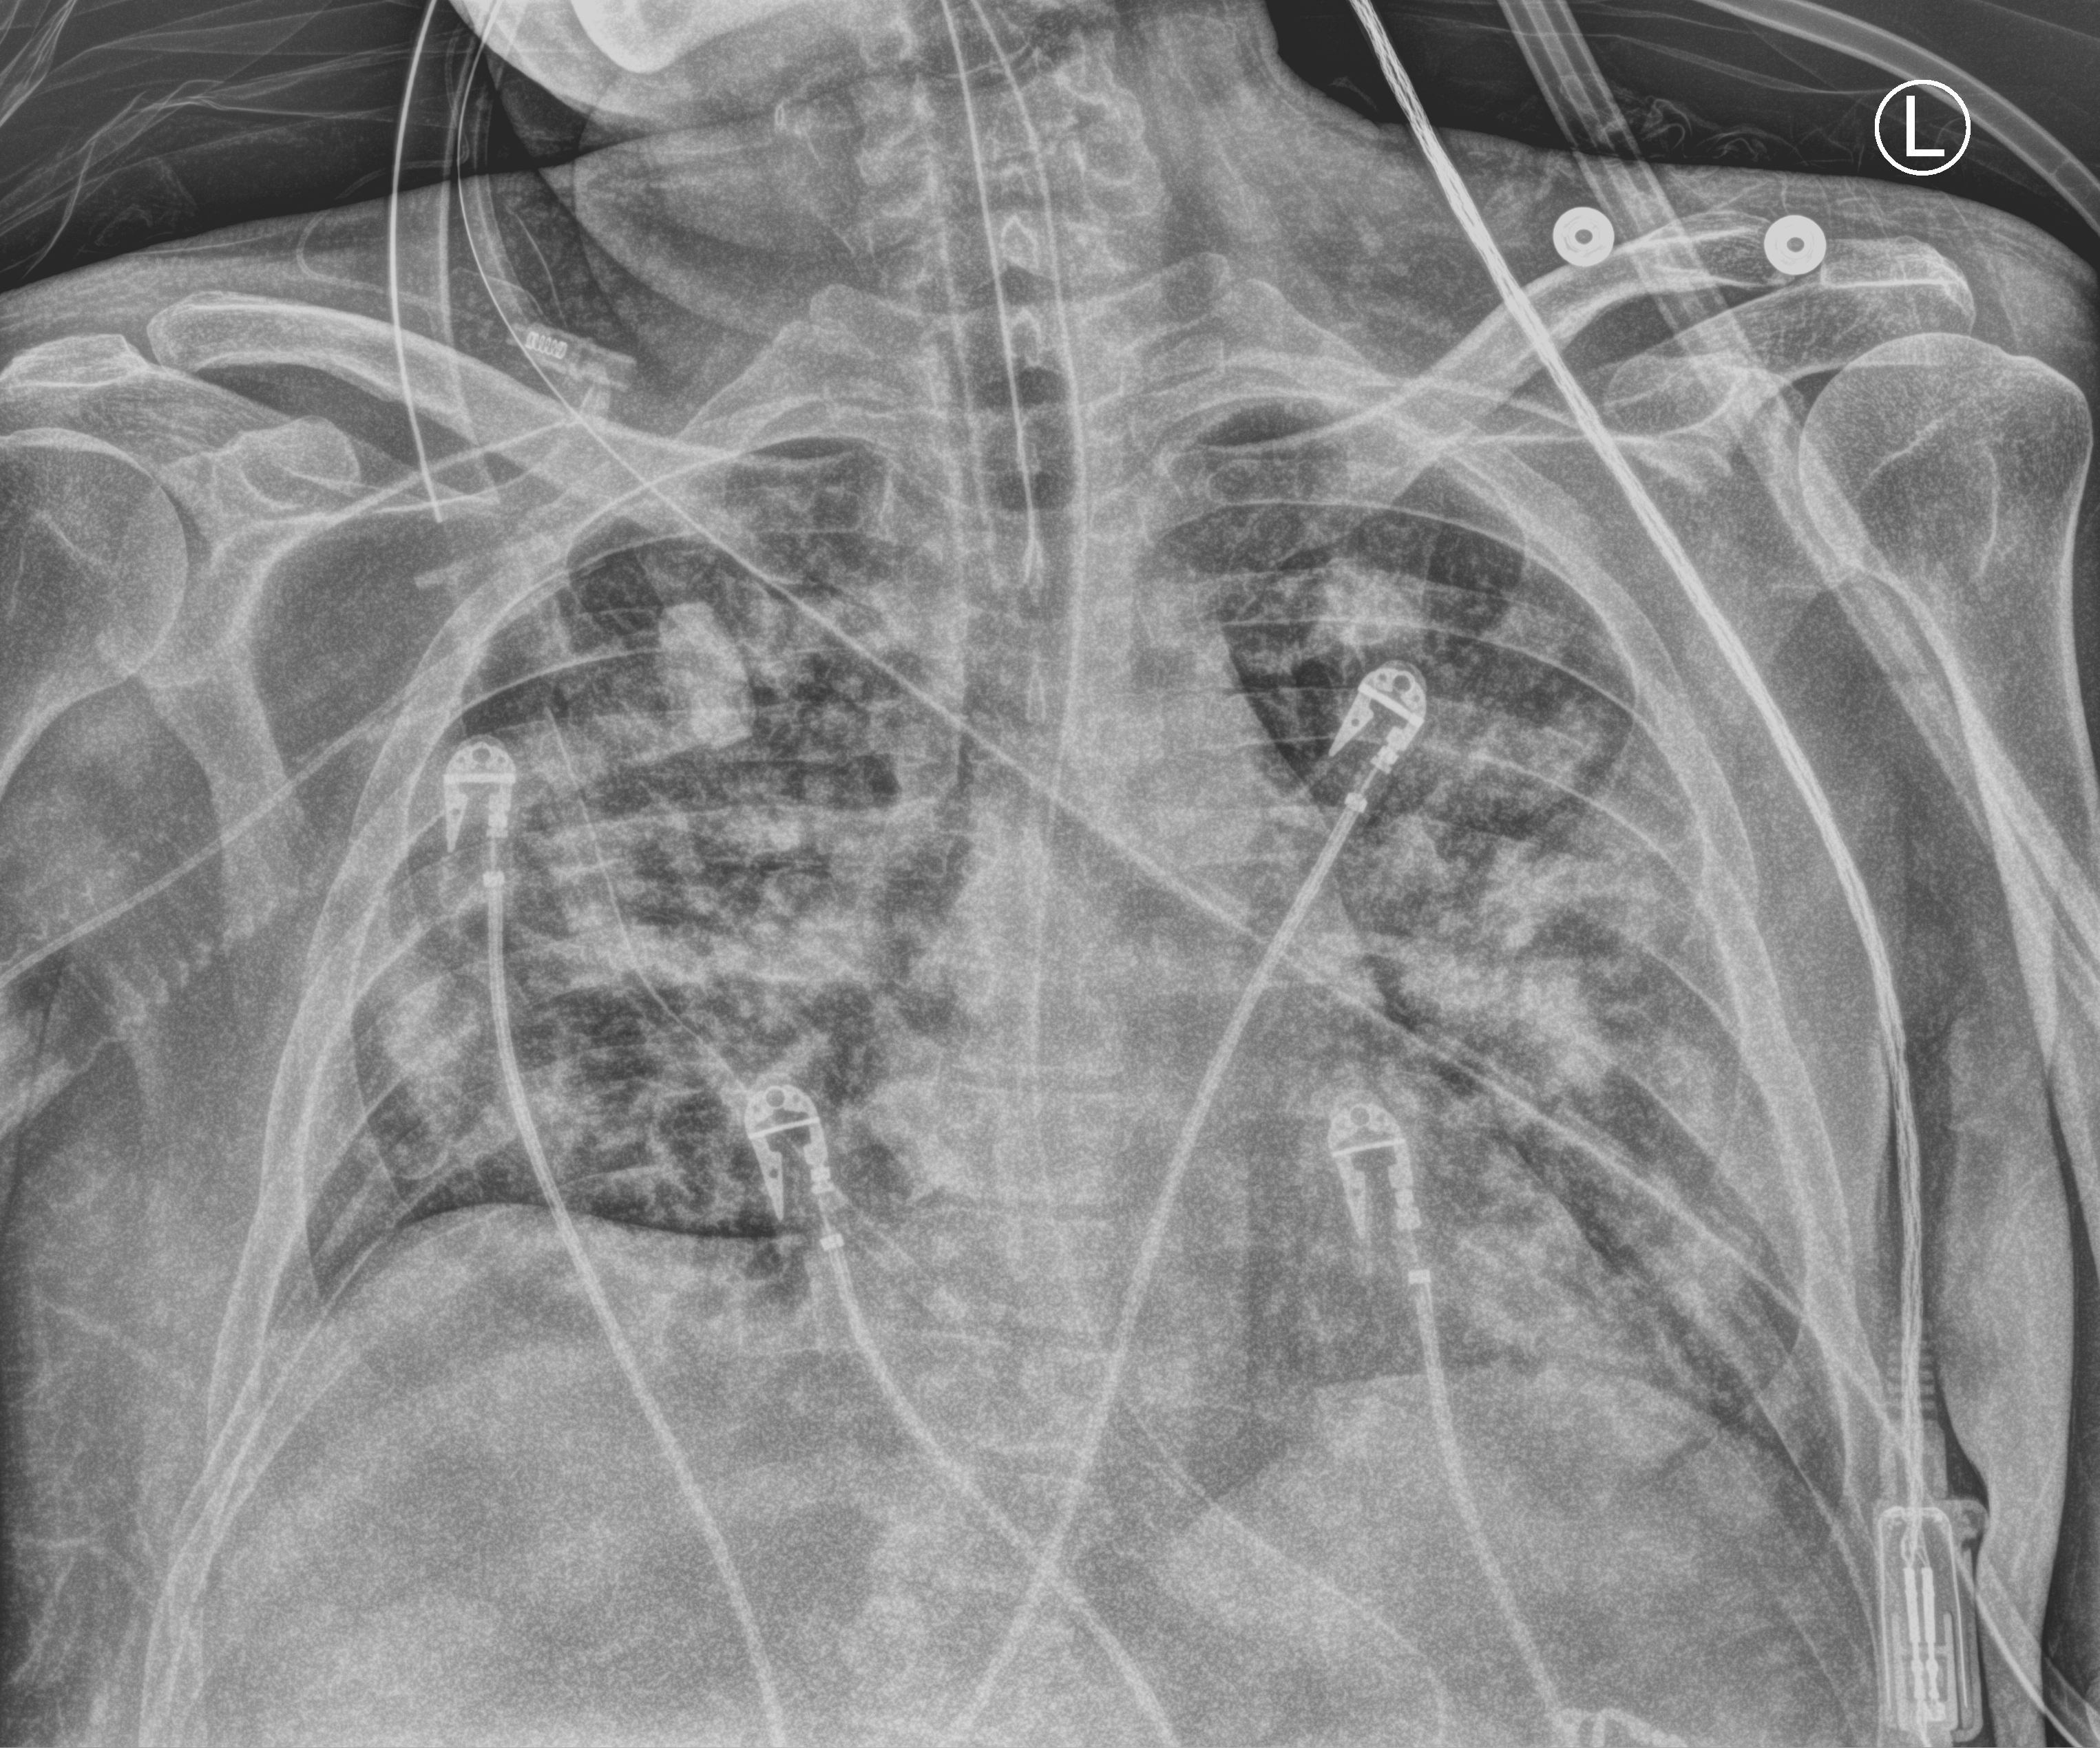
Portable chest radiograph, anteroposterior (AP) projection. Patient hospitalised with COVID-19; male, aged 18–59 years.
From the hospital-stay record, not from the radiograph (when in the stay this image was taken is not recorded):
- mechanically ventilated during this hospital stay: yes